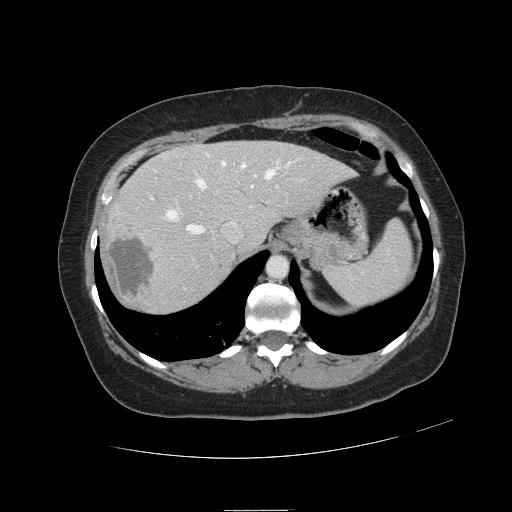
Contrast-enhanced abdominal CT, one axial slice; slice 90 of 121 in the series (ordered by position); intravenous contrast given; soft-tissue window (W 400 / L 40 HU); 2.5 mm slice thickness; 512 × 512 image matrix. Female patient, age 52 years. From the clinical record (not read from this slice): diagnosis: colorectal cancer liver metastases, imaged before liver resection; multiple liver metastases: yes; largest metastasis: 6.3 cm; disease in both lobes: no.
Structures marked on this image (outlined manually by an expert reader):
- hepatic veins: bounding box (x1, y1, x2, y2) in pixels: (167, 154, 291, 234)
- liver: (105, 141, 352, 312)
- planned liver remnant (the part of the liver to remain after resection): (168, 142, 352, 248)
- portal vein (with intrahepatic branches): (150, 186, 278, 290)
- liver metastasis: (107, 235, 155, 298)